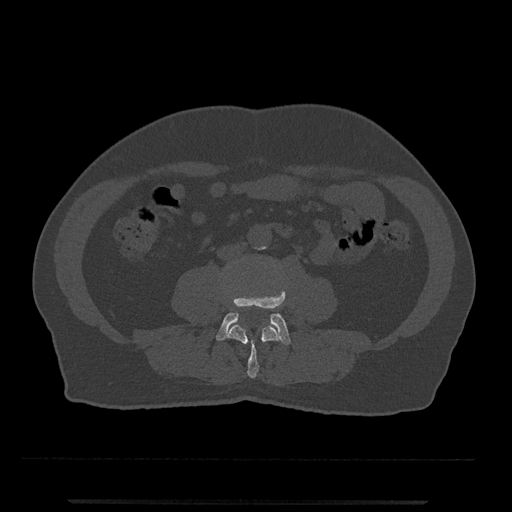
CT including the spine, one axial slice. Position 168 of 797 along the scan axis. Reconstruction kernel Br40s/3. Bone window (W 1800 / L 400 HU). 0.5 mm slice thickness. 512 × 512 image matrix, field of view 419 × 419 mm. Male patient, age 63 years. From the clinical record (not read from this slice): primary cancer: prostate.
Annotated regions visible in this slice (semi-automatically segmented with operator editing):
- L3 vertebra: box from (x=227, y=306) to (x=281, y=378) px
- L4 vertebra: (x=216, y=290)–(x=291, y=345)